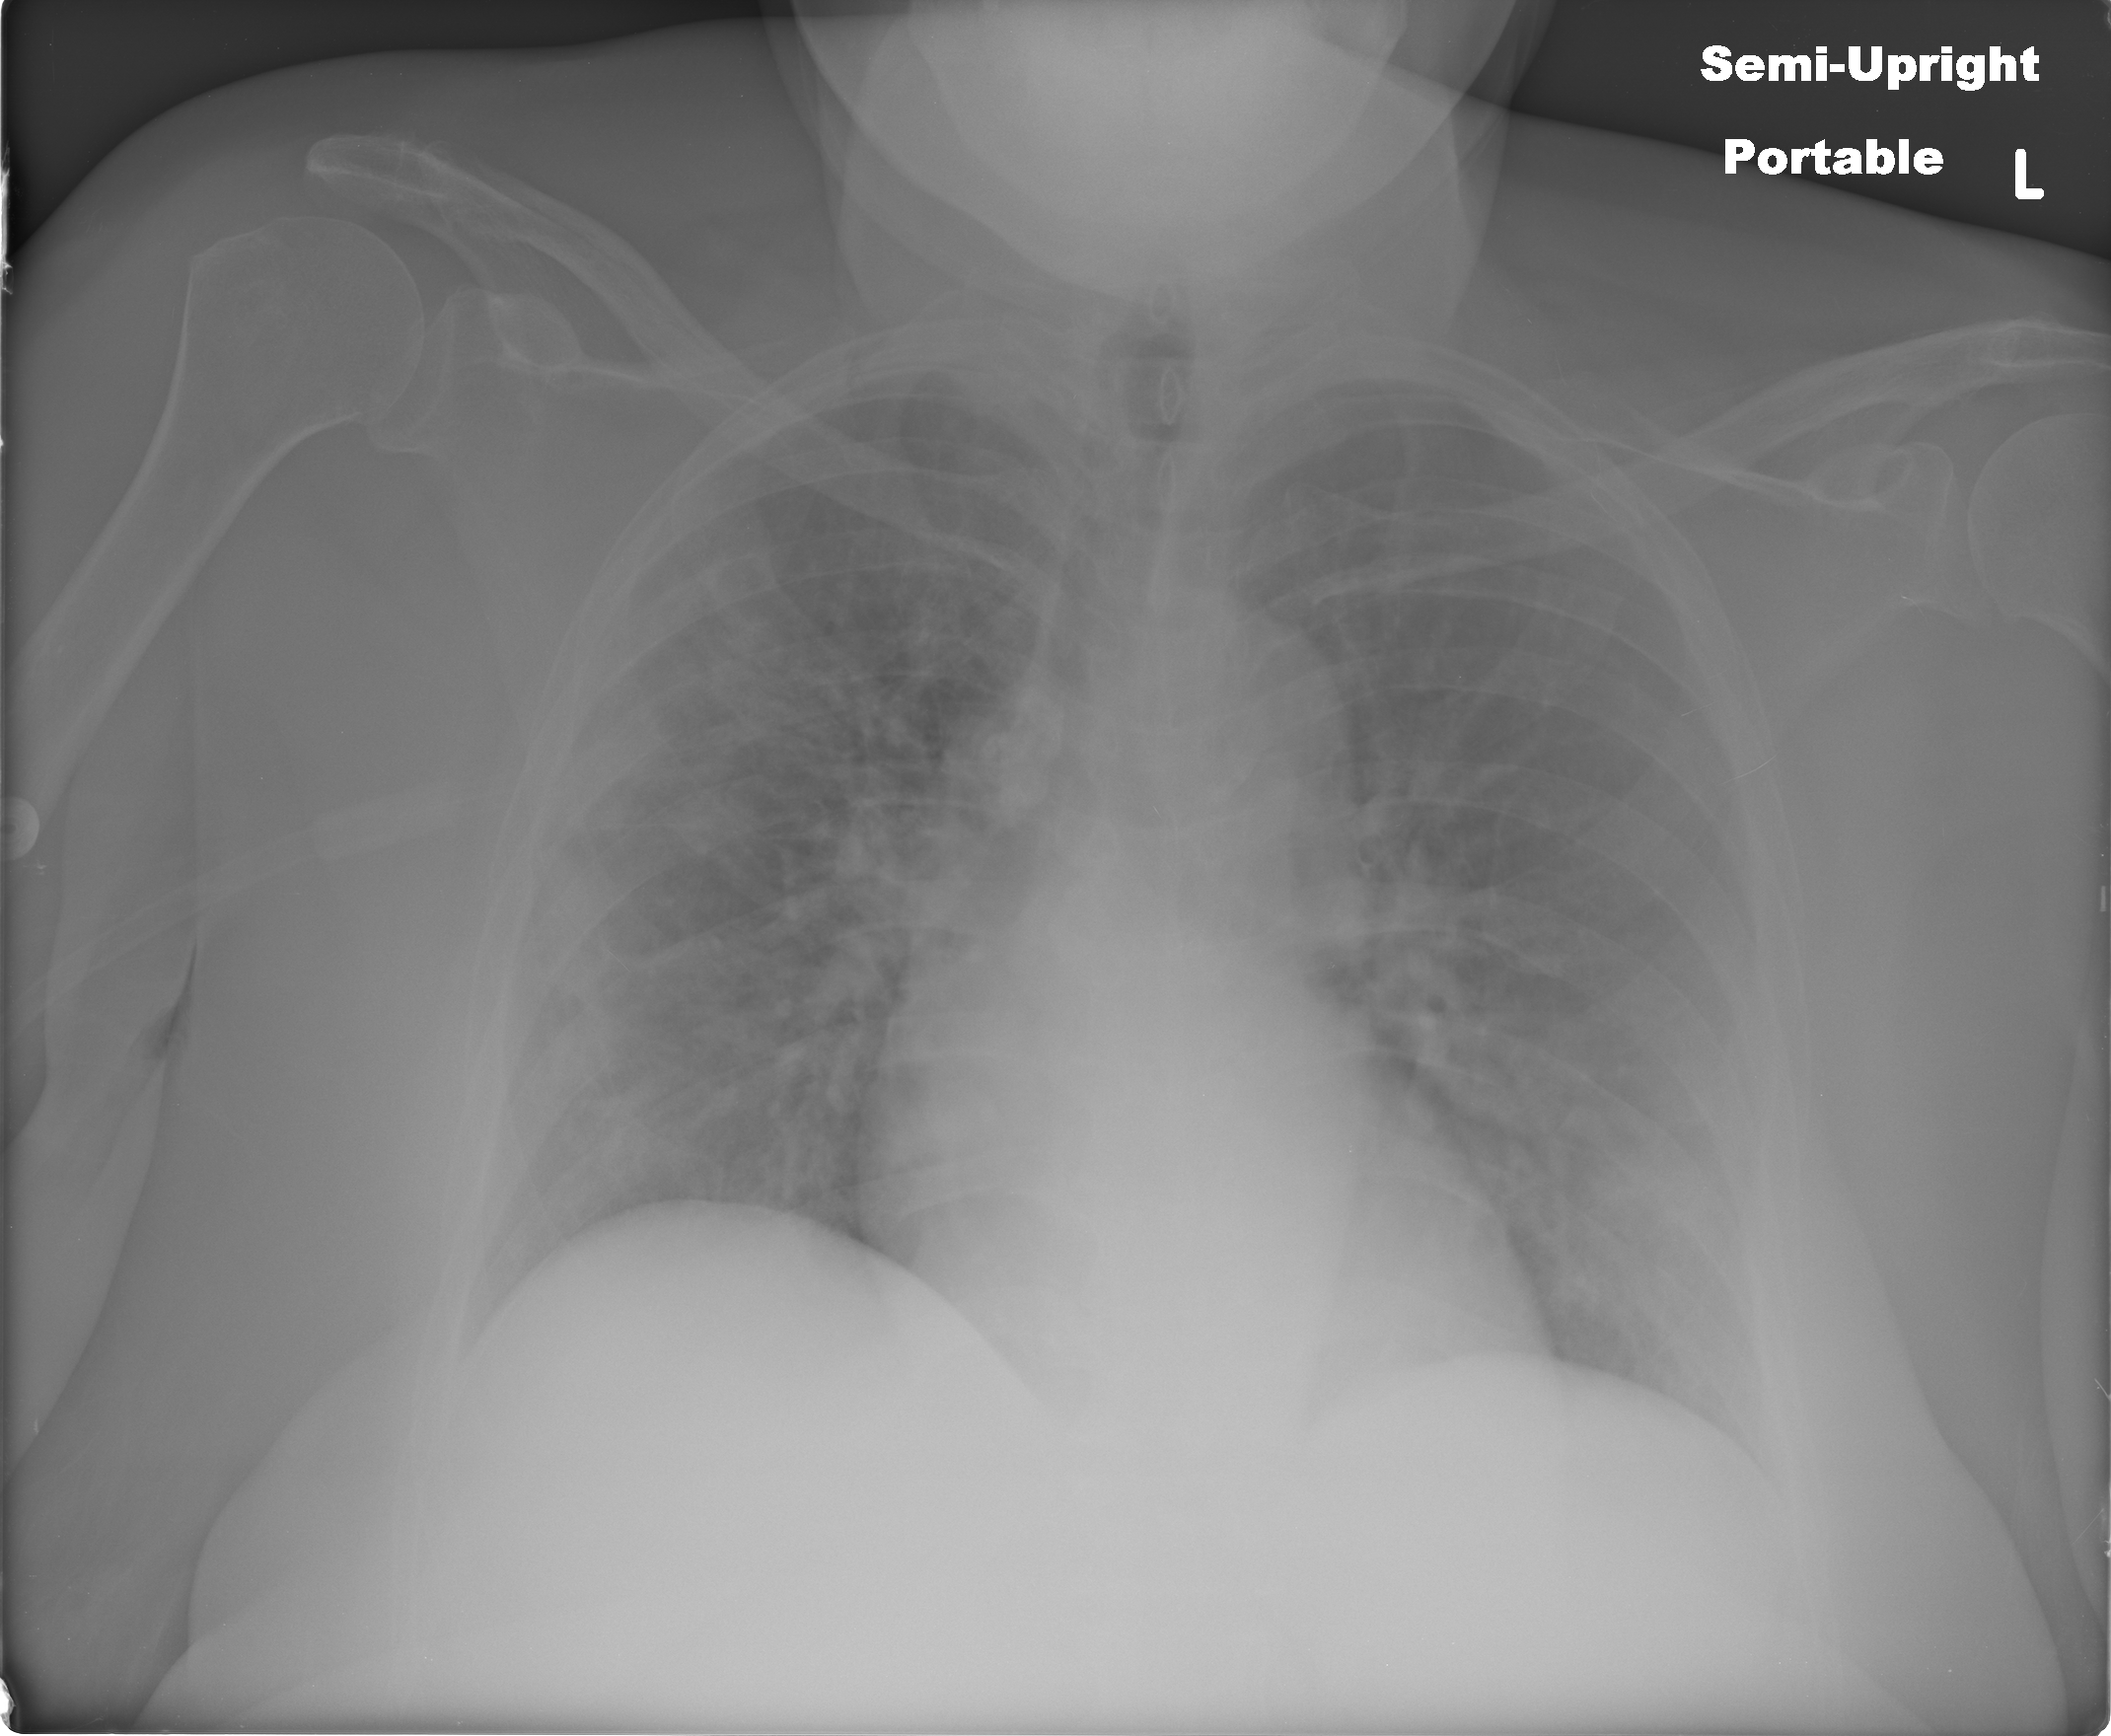
Chest X-ray (portable), AP projection. Female patient, age 59 years; COVID-19 (test-positive).
Key findings recorded by the radiologist: subtle increased perihilar hazy airspace opacities bilaterally.